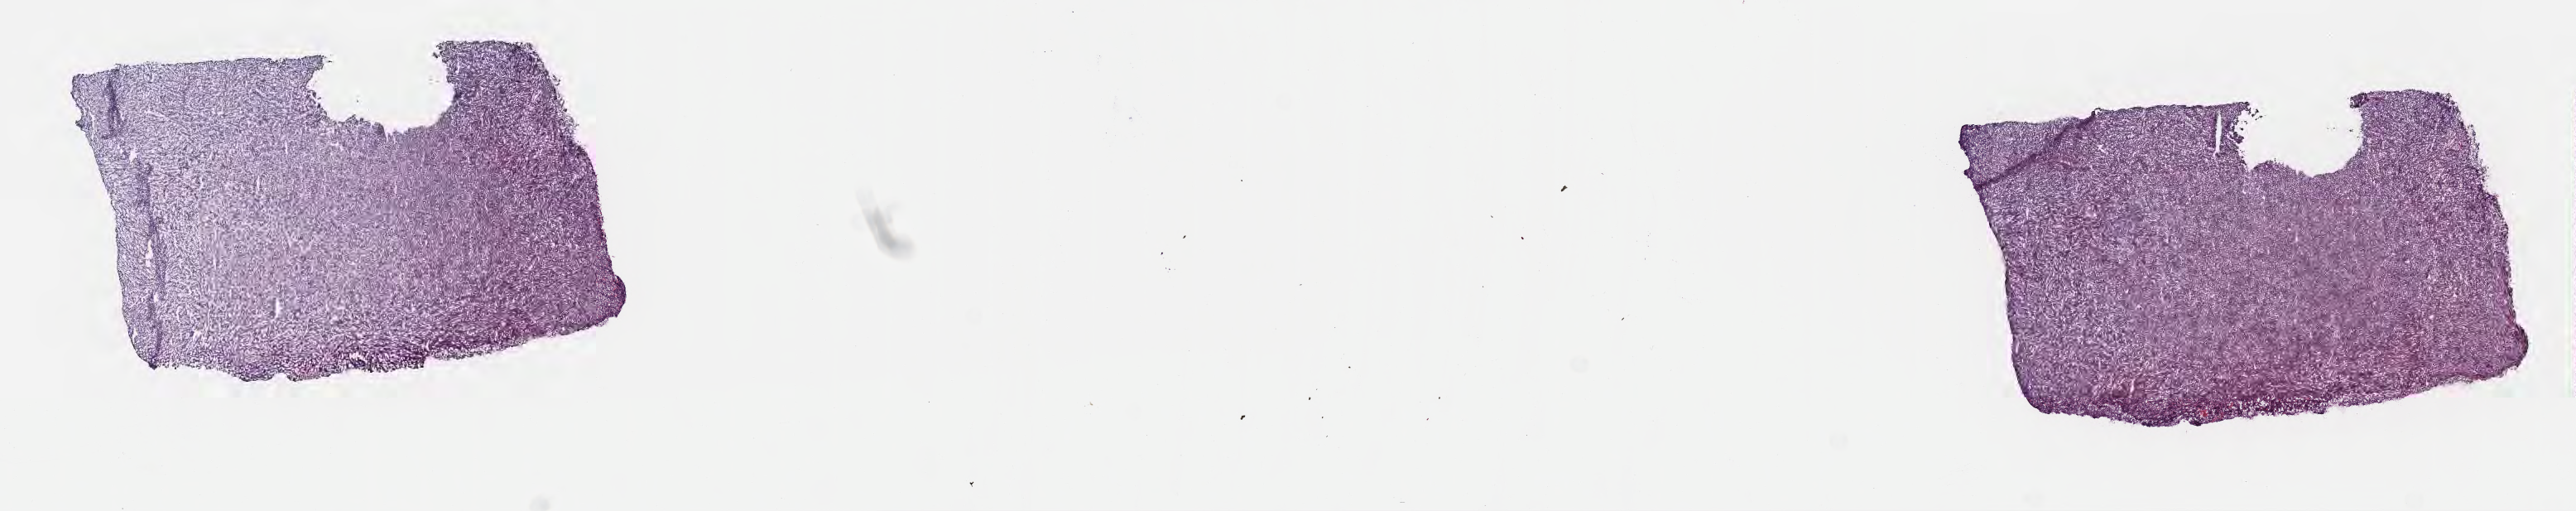
Digitized hematoxylin and eosin (H&E)-stained section, shown as a low-resolution overview of the whole scanned area (about 25.2 x 5.0 mm). Frozen section. Primary tumor. Anatomic site: cranium. Male patient; age at initial diagnosis 8 years. Composition of this section per pathologist review: tumor cells 90%, tumor nuclei 90%, stromal cells 5%, necrosis 5%, normal cells 0%. Infiltration values recorded for this section: lymphocyte infiltration 50%, monocyte infiltration 25%, neutrophil infiltration 5%.
Diagnosis: Burkitt lymphoma, NOS. Ann Arbor stage (patient): Stage I.